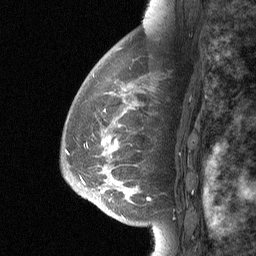
Breast MRI (dynamic contrast-enhanced), one sagittal slice. Slice 45 of 64 in the series (ordered by position). Dynamic contrast-enhanced study with each time point stored as its own series, time point 2 of 3 at this slice position (early post-contrast, ordered by acquisition time). 1.5 T. TE 4.8 ms, TR 27 ms. 2 mm slice thickness. 256 × 256 image matrix, field of view 180 × 180 mm. Patient: female, 56 years. Case-level facts recorded for this patient, not image findings: setting: breast cancer imaged before/during neoadjuvant chemotherapy; receptor status: HER2-positive.
Outlined on this slice (semi-automatically segmented with operator editing):
- analysis volume of interest (the breast-tissue region the enhancement analysis was run in; not a lesion): box from (x=90, y=83) to (x=162, y=214) px
- tumour enhancement mask (voxels above the 90 % enhancement threshold inside the analysis volume of interest): (x=124, y=189)–(x=127, y=197)